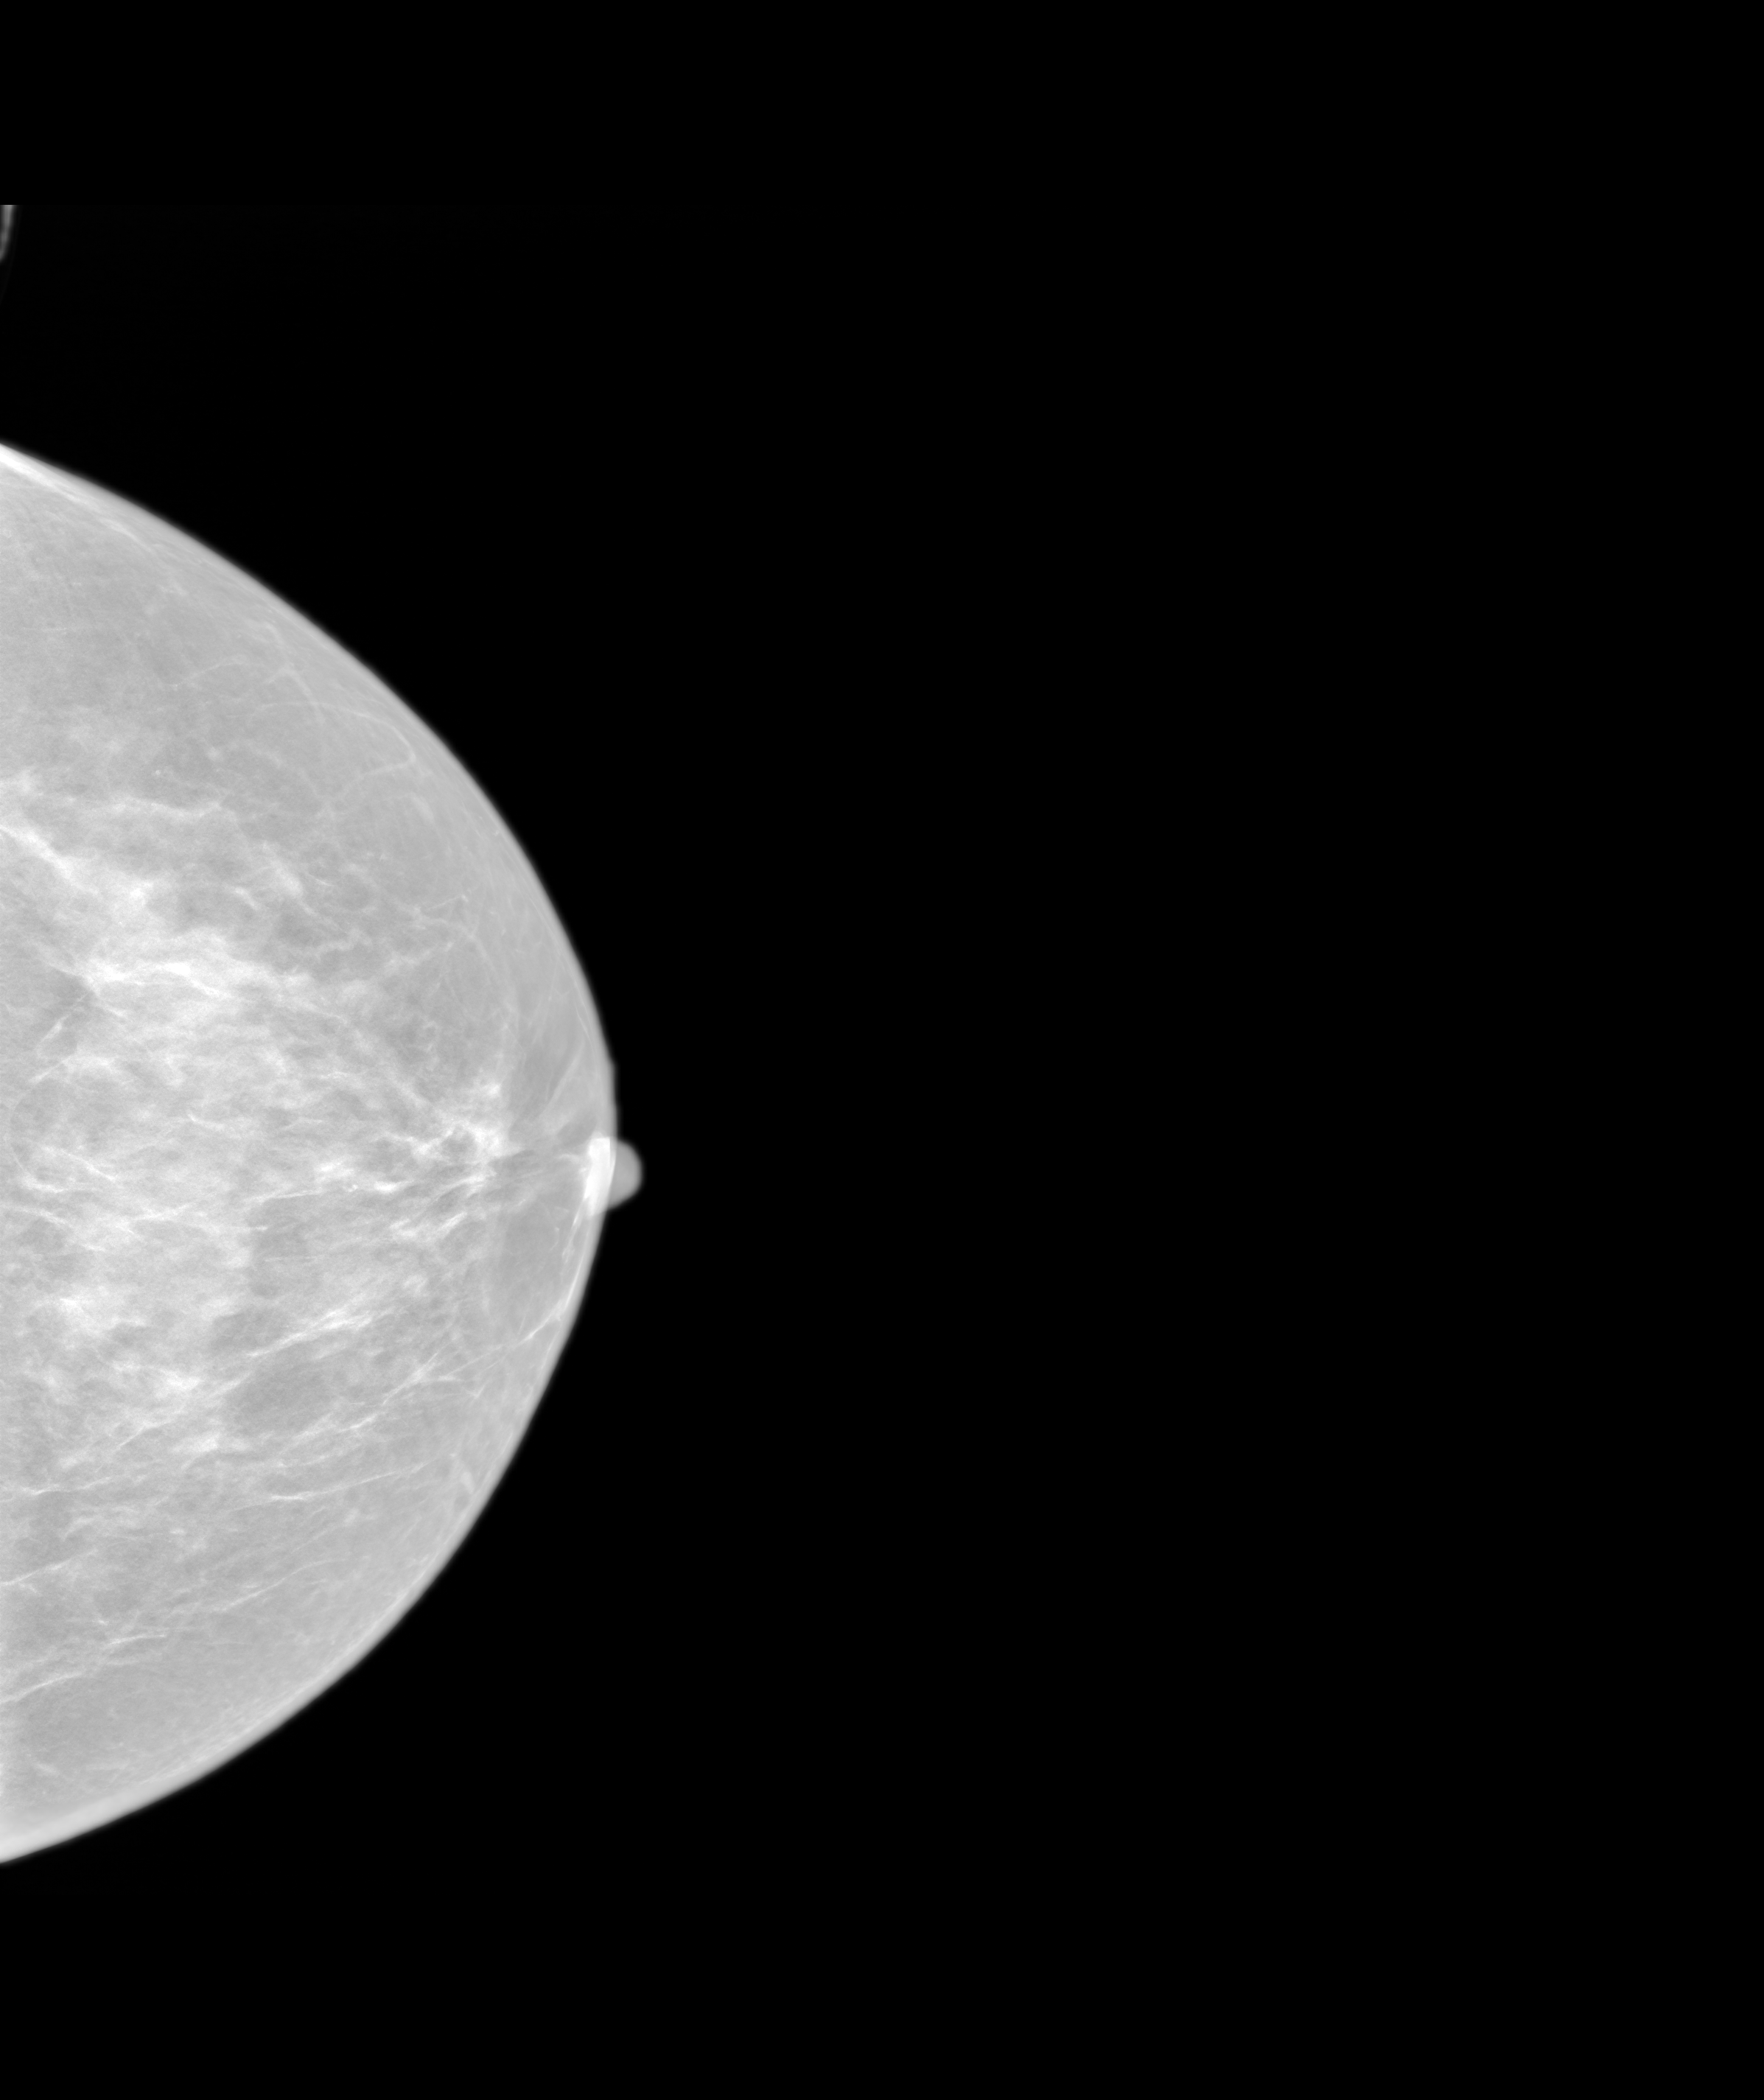
Synthesized 2-D mammogram reconstructed from digital breast tomosynthesis; left breast; cranio-caudal projection; annual screening mammography examination. Patient aged 48 years (female).
Final BI-RADS assessment for this screening round (tomosynthesis exam, both breasts): category 1.